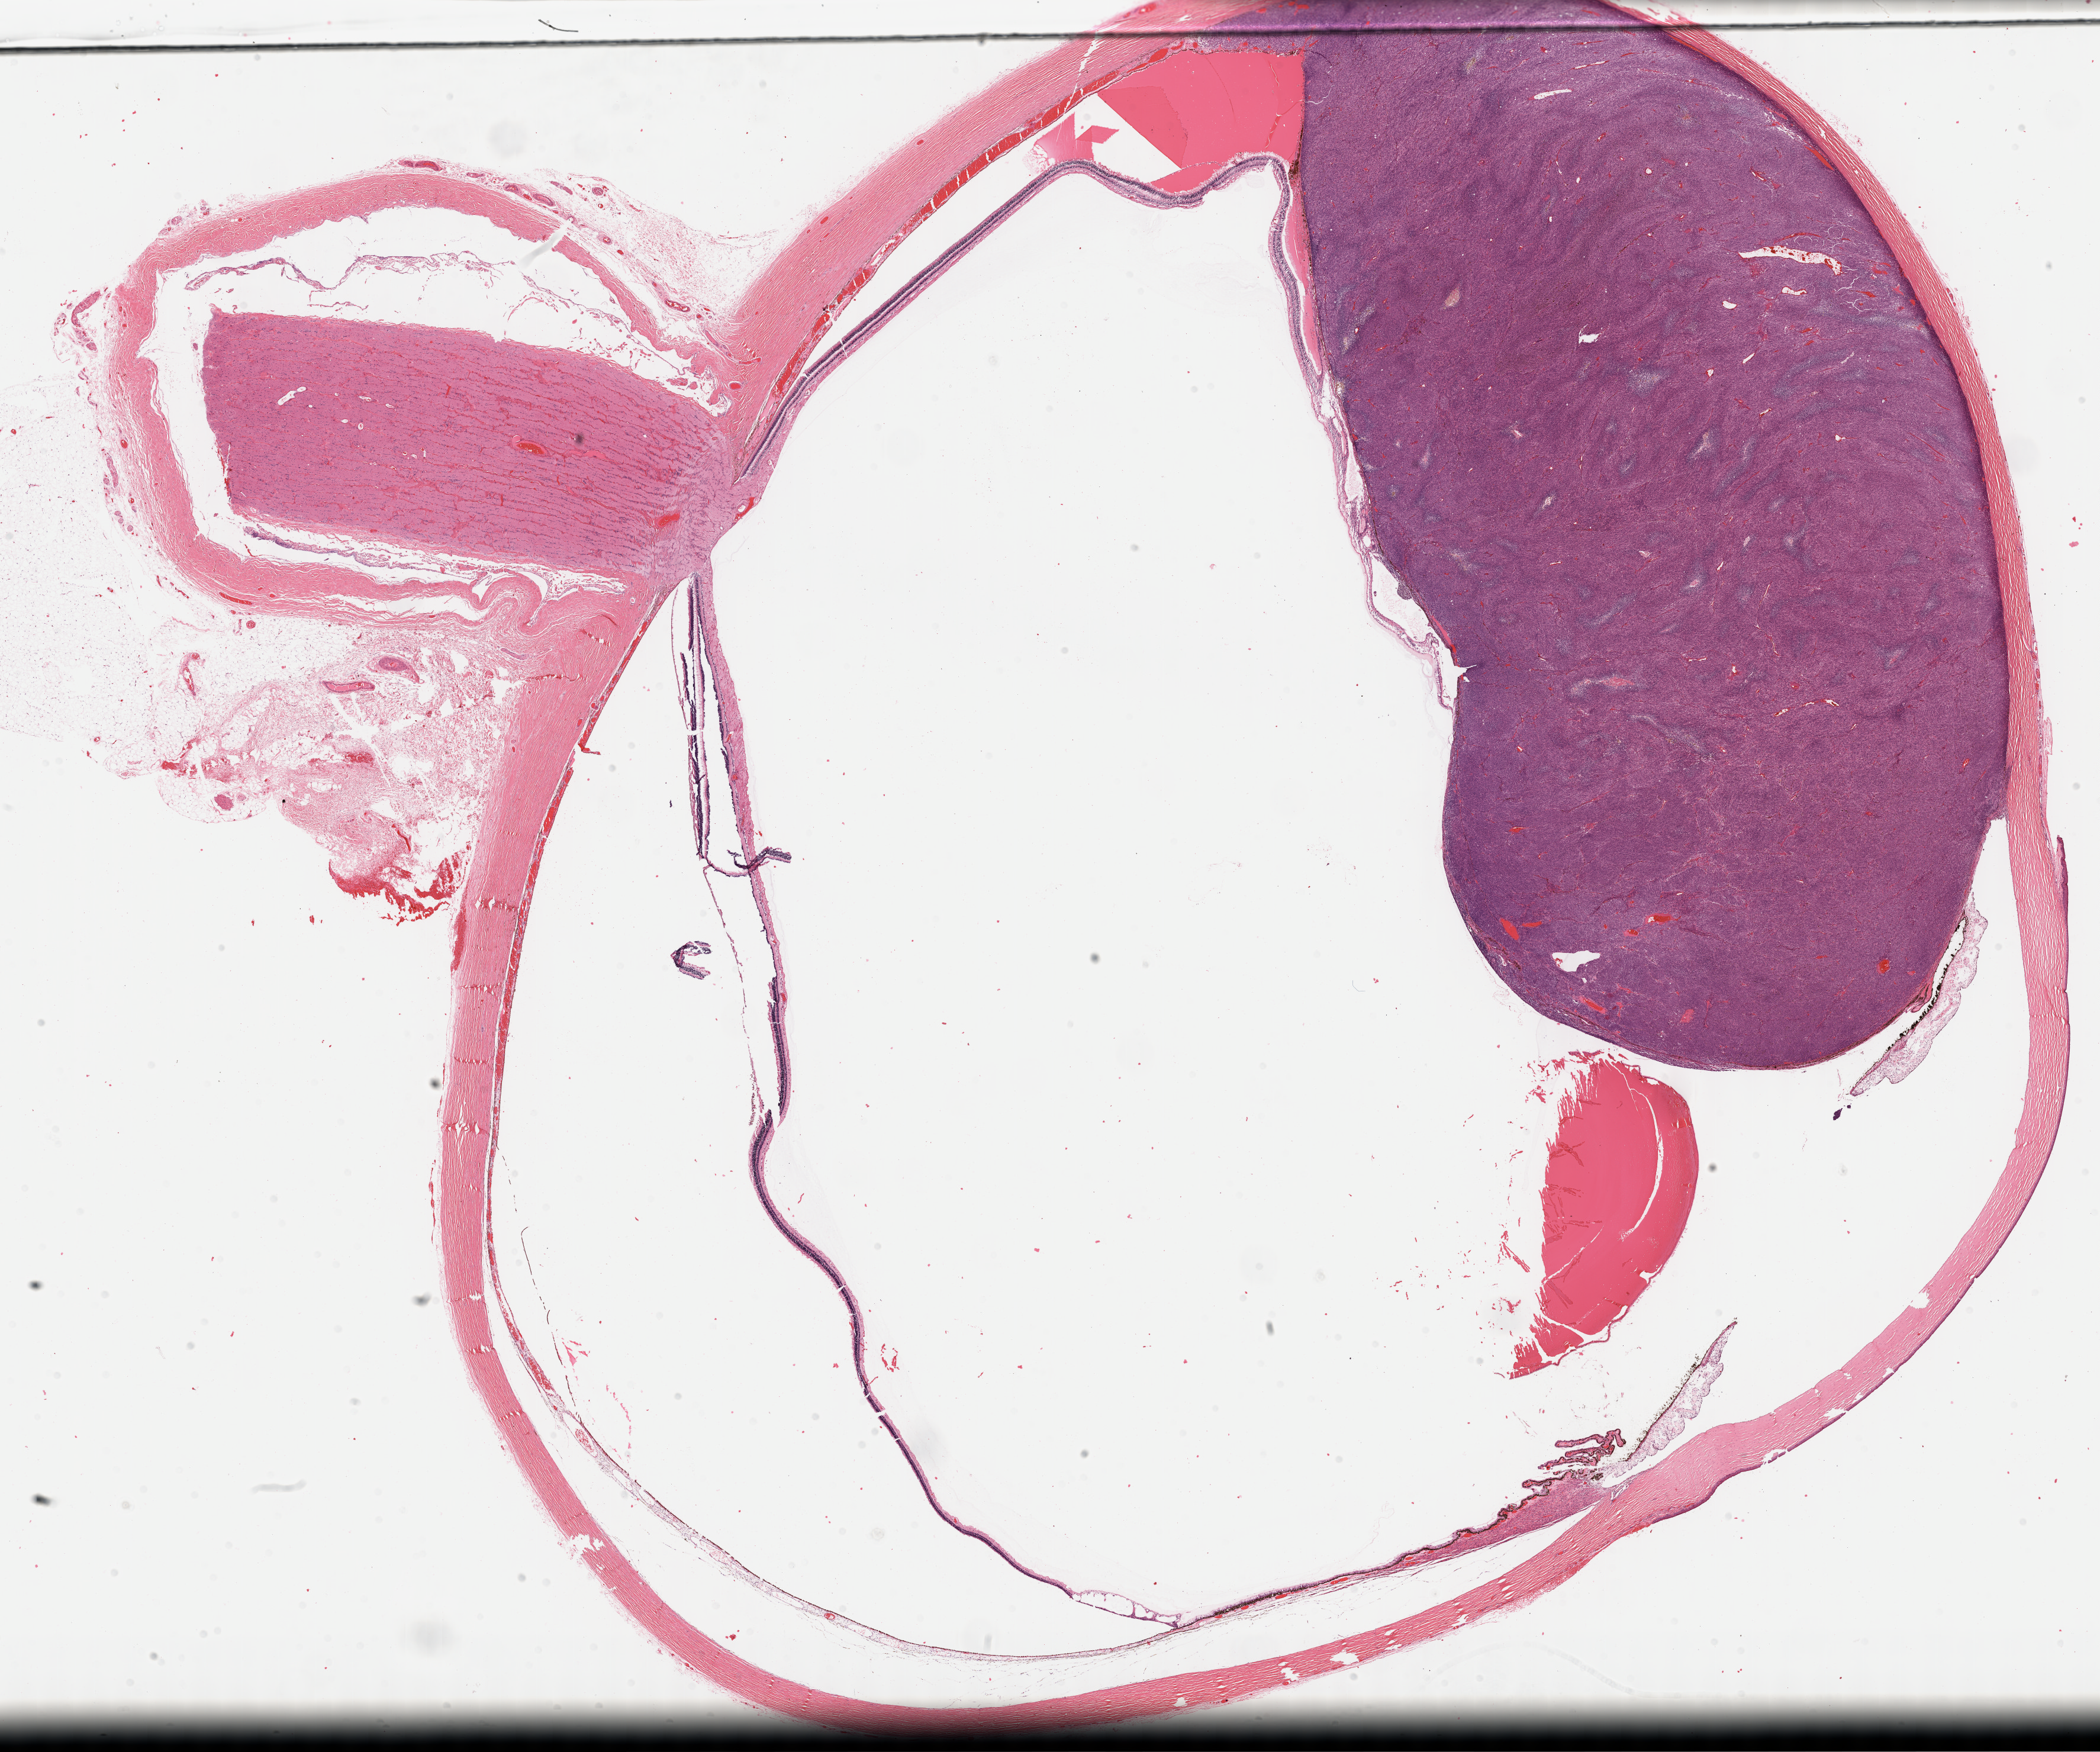
Digitized H&E tissue section (whole slide) — whole scanned area (about 28.7 x 23.9 mm, acquisition: 40x scan) shown as a low-resolution overview. FFPE section. Sample: primary tumour, uvea. Female, age 47 years at initial diagnosis.
- histologic diagnosis: Mixed epithelioid and spindle cell melanoma (overlapping lesion of eye and adnexa)
- AJCC pathologic stage: IV (7th edition)